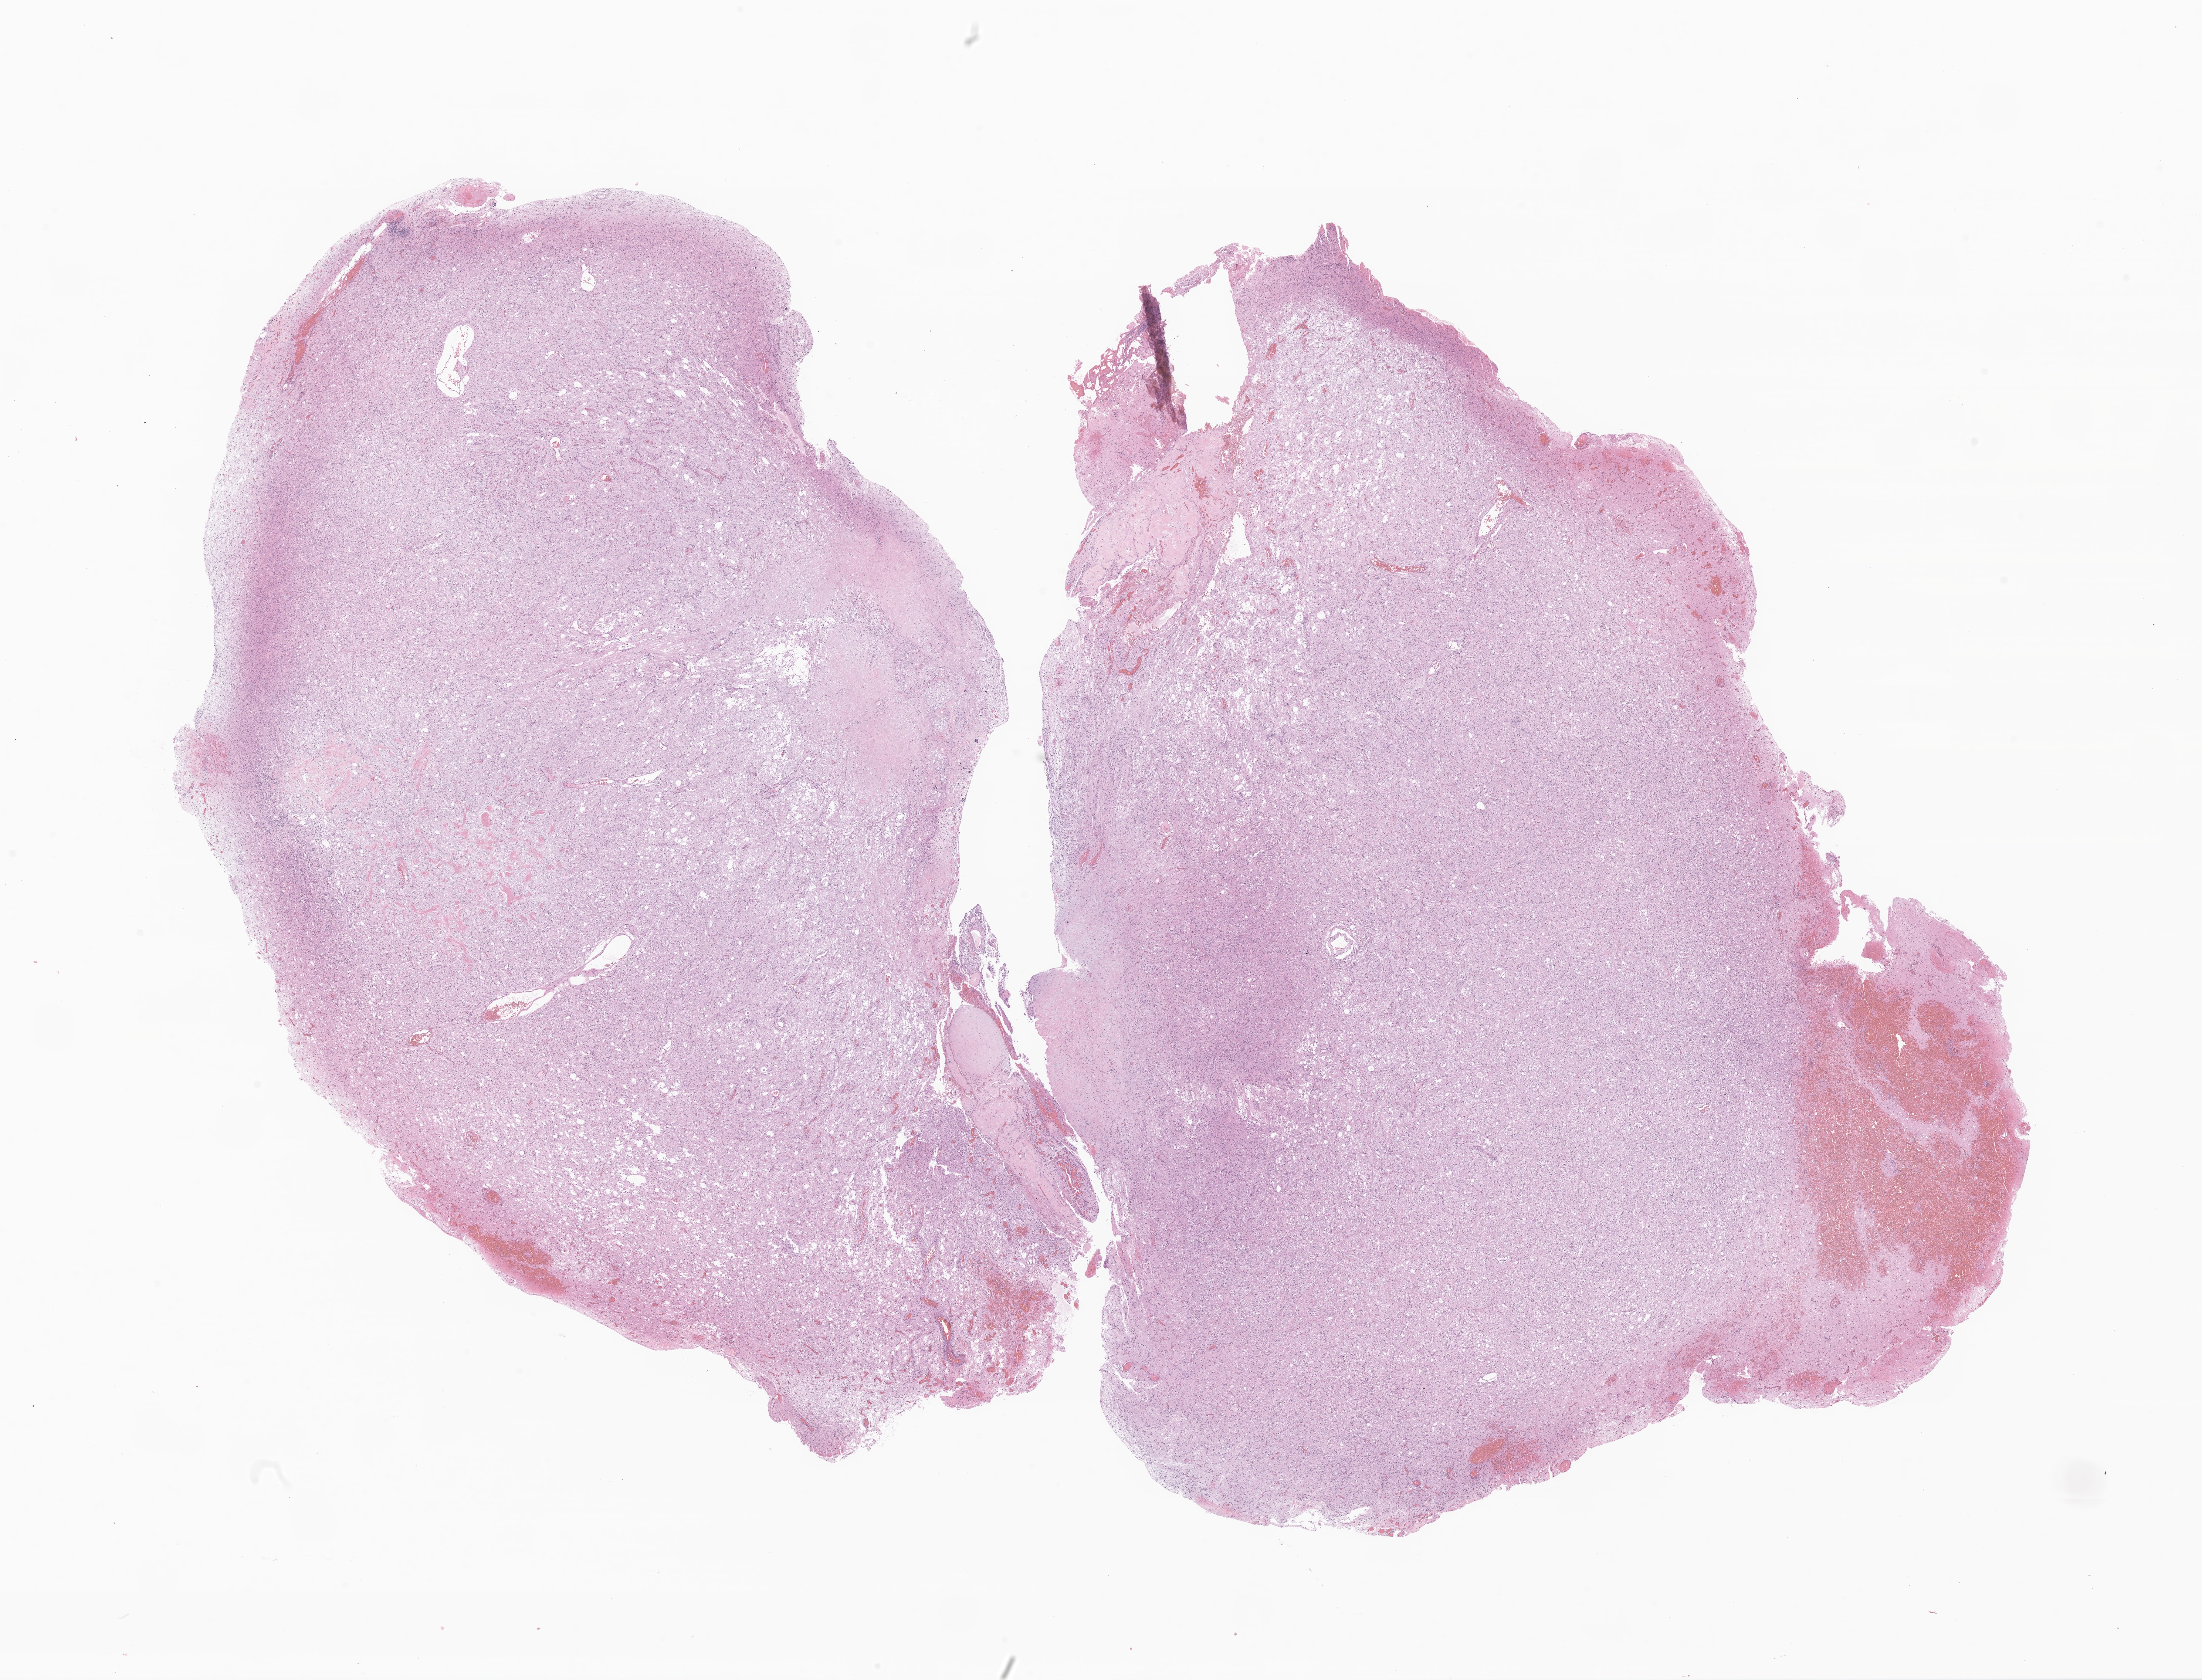
H&E whole-slide image of tumor tissue from the cerebellum — whole scanned area (about 25.1 x 19.2 mm) shown as a low-resolution overview, FFPE section. Patient male; age 208 months (17 years 4 months).
Recorded diagnosis: Ganglioglioma, NOS.